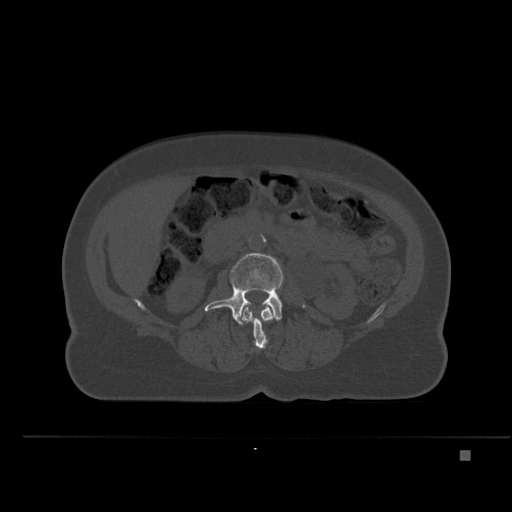
CT including the spine, one axial slice. Slice 204 of 477 in the series (ordered by position). Bone window (W 1800 / L 400 HU). 1.5 mm slice thickness. 512 × 512 image matrix, field of view 422 × 422 mm. Patient: female, 74 years. From the clinical record (not read from this slice): primary cancer: colon.
Outlined on this slice (semi-automatic segmentation, software-assisted and operator-edited):
- L2 vertebra: box from (x=242, y=304) to (x=273, y=349) px
- L3 vertebra: (x=204, y=253)–(x=283, y=325)